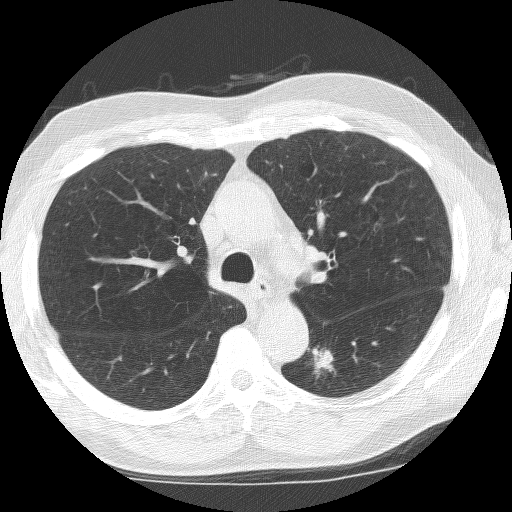
Low-dose screening chest CT, one axial slice; position 101 of 155 along the scan axis; 120 kVp; lung window (W 1500 / L -600 HU); 2.5 mm slice thickness; 512 × 512 image matrix.
Structures marked on this image (outlined manually by an expert reader):
- lesion 1 (tumor, lower lobe of left lung): bounding box <309,346,336,379> (left, top, right, bottom; pixels)